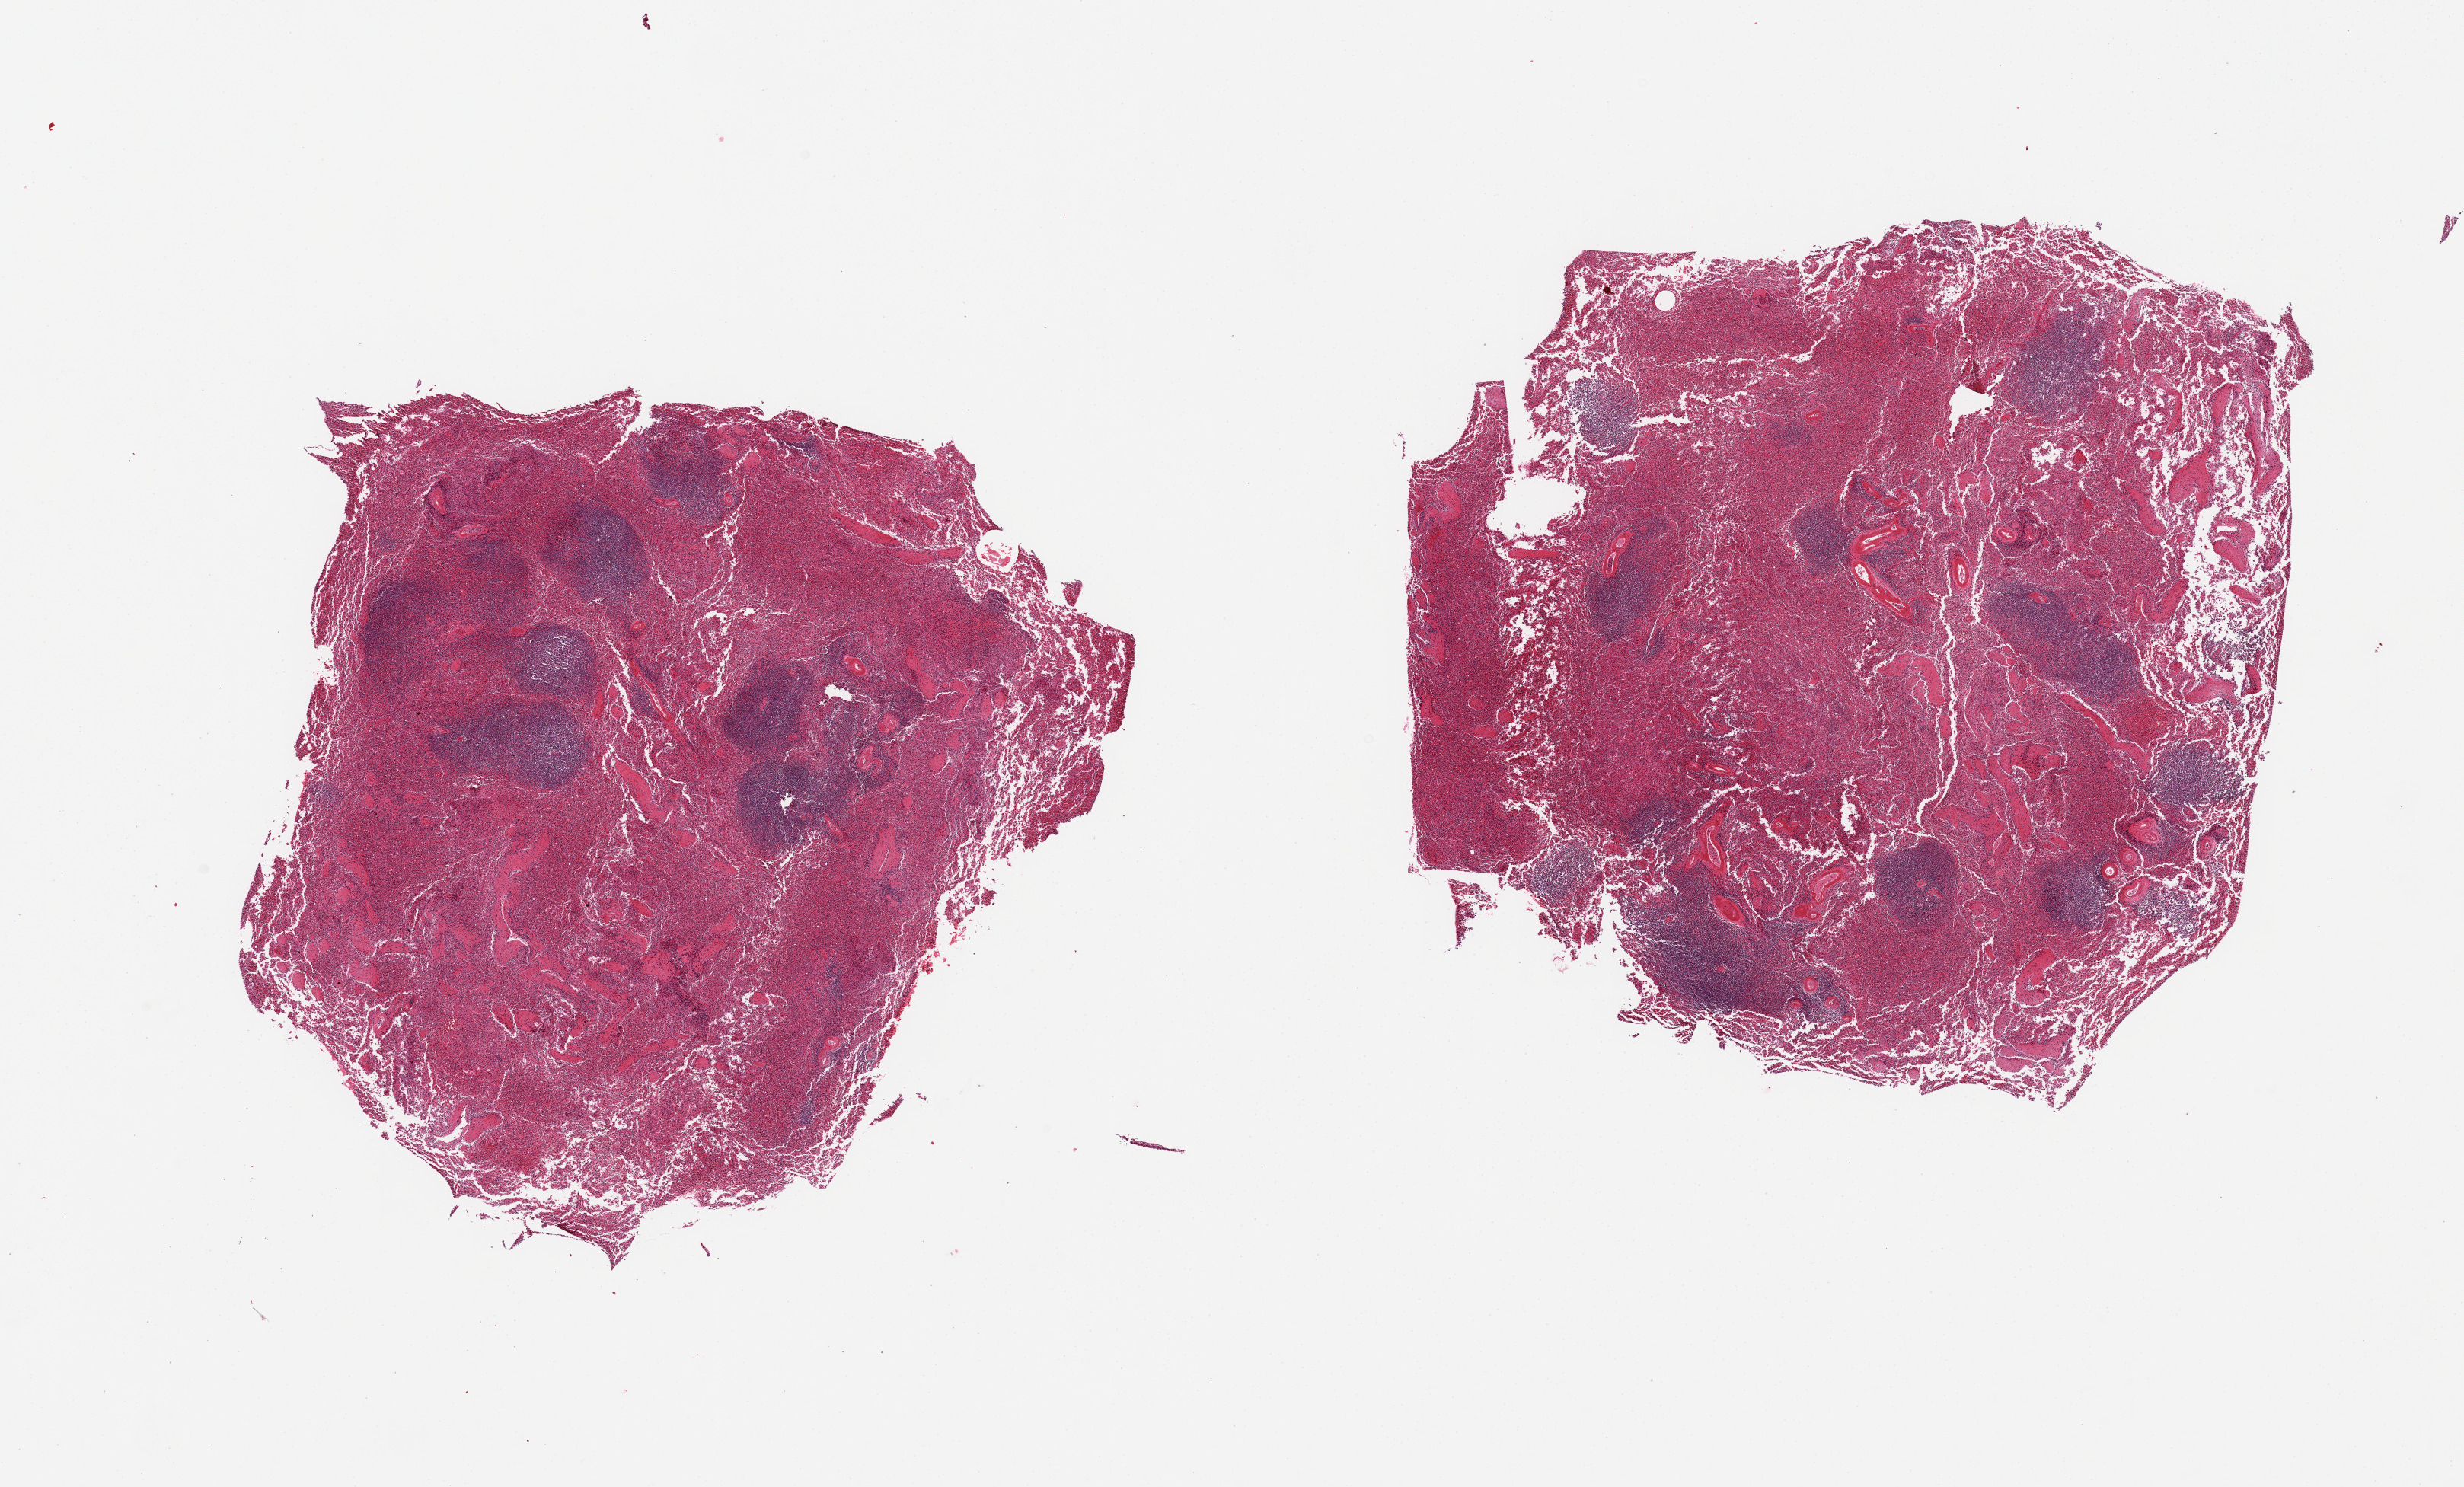
H&E whole-slide image — low-resolution overview of the scanned area, about 25.6 x 15.4 mm (from a 20x scan), PAXgene-fixed paraffin-embedded (PFPE) section, sampled site (target tissue): spleen, donor tissue sample. Female donor.
Pathologist's review note for this sample: 2 pieces.